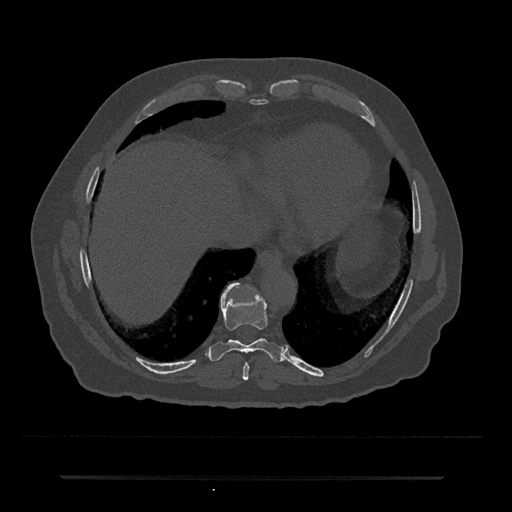
CT including the spine, one axial slice; slice 279 of 797 in the series (ordered by position); reconstruction kernel Br40s/3; bone window (W 1800 / L 400 HU); 0.5 mm slice thickness; 512 × 512 image matrix, field of view 437 × 437 mm. Patient: male, 69 years. Case-level facts recorded for this patient, not image findings: primary cancer: prostate.
Outlined on this slice (semi-automatically segmented with operator editing):
- T8 vertebra: bounding box [x1, y1, x2, y2] px = [242, 363, 249, 380]
- T9 vertebra: [210, 283, 284, 362]